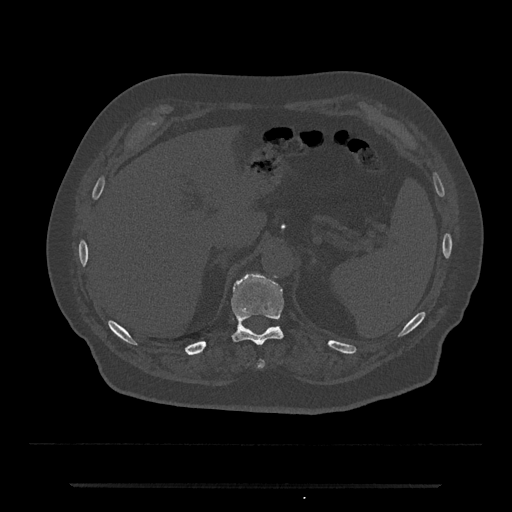
CT including the spine, one axial slice; slice 649 of 797 in the series (ordered by position); reconstruction kernel Br40s/3; bone window (W 1800 / L 400 HU); 0.5 mm slice thickness; 512 × 512 image matrix, field of view 434 × 434 mm. Male patient, age 80 years. From the clinical record (not read from this slice): primary cancer: prostate.
Outlined on this slice (semi-automatic segmentation, software-assisted and operator-edited):
- T10 vertebra: bounding box <258,360,265,367> (left, top, right, bottom; pixels)
- T11 vertebra: <231,274,285,346>